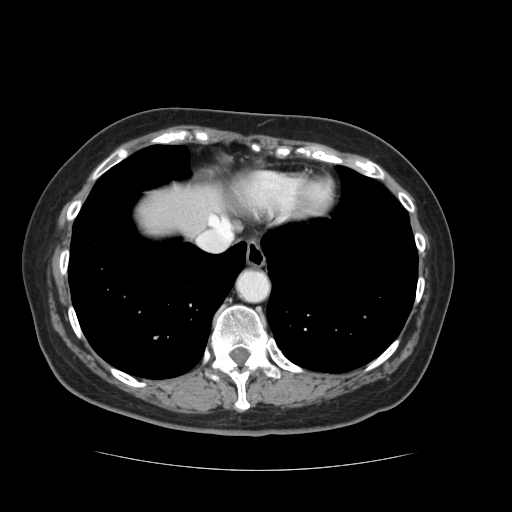
Contrast-enhanced abdominal CT, one axial slice; slice 115 of 128 in the series (ordered by position); 120 kVp; intravenous contrast given; soft-tissue window (W 400 / L 40 HU); 2.5 mm slice thickness; 512 × 512 image matrix, field of view 366 × 366 mm. Female patient, age 67 years. Case-level facts recorded for this patient, not image findings: diagnosis: colorectal cancer liver metastases, imaged before liver resection; multiple liver metastases: yes; largest metastasis: 3 cm.
Structures marked on this image (manually delineated by an expert):
- hepatic veins: bounding box [x1, y1, x2, y2] px = [210, 216, 230, 230]
- liver: [139, 184, 220, 235]
- planned liver remnant (the part of the liver to remain after resection): [140, 192, 221, 236]